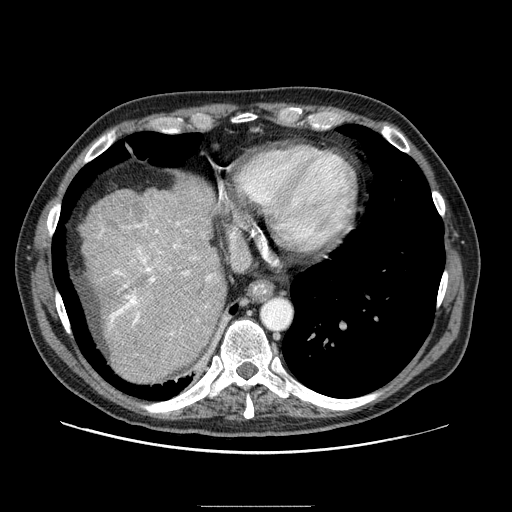
Contrast-enhanced abdominal CT (liver protocol), one axial slice; slice 76 of 99 in the series (ordered by position); 100 kVp; one of 2 acquisitions stored at this slice position; soft-tissue window (W 400 / L 40 HU); 512 × 512 image matrix, field of view 400 × 400 mm. From the clinical record (not read from this slice): diagnosis: hepatocellular carcinoma (patient treated with transarterial chemoembolisation; whether this scan precedes or follows treatment is not stated here); TNM stage (as recorded): Stage-II; Child-Pugh class: A; tumour differentiation: well differentiated; tumour nodularity: multinodular.
Outlined on this slice (semi-automatic segmentation, software-assisted and operator-edited):
- liver parenchyma outside the tumour (the mass and vessels are separate outlines, so this box may not span the whole liver): bounding box (x1, y1, x2, y2) in pixels: (82, 180, 226, 382)
- liver vessels: (100, 222, 213, 335)